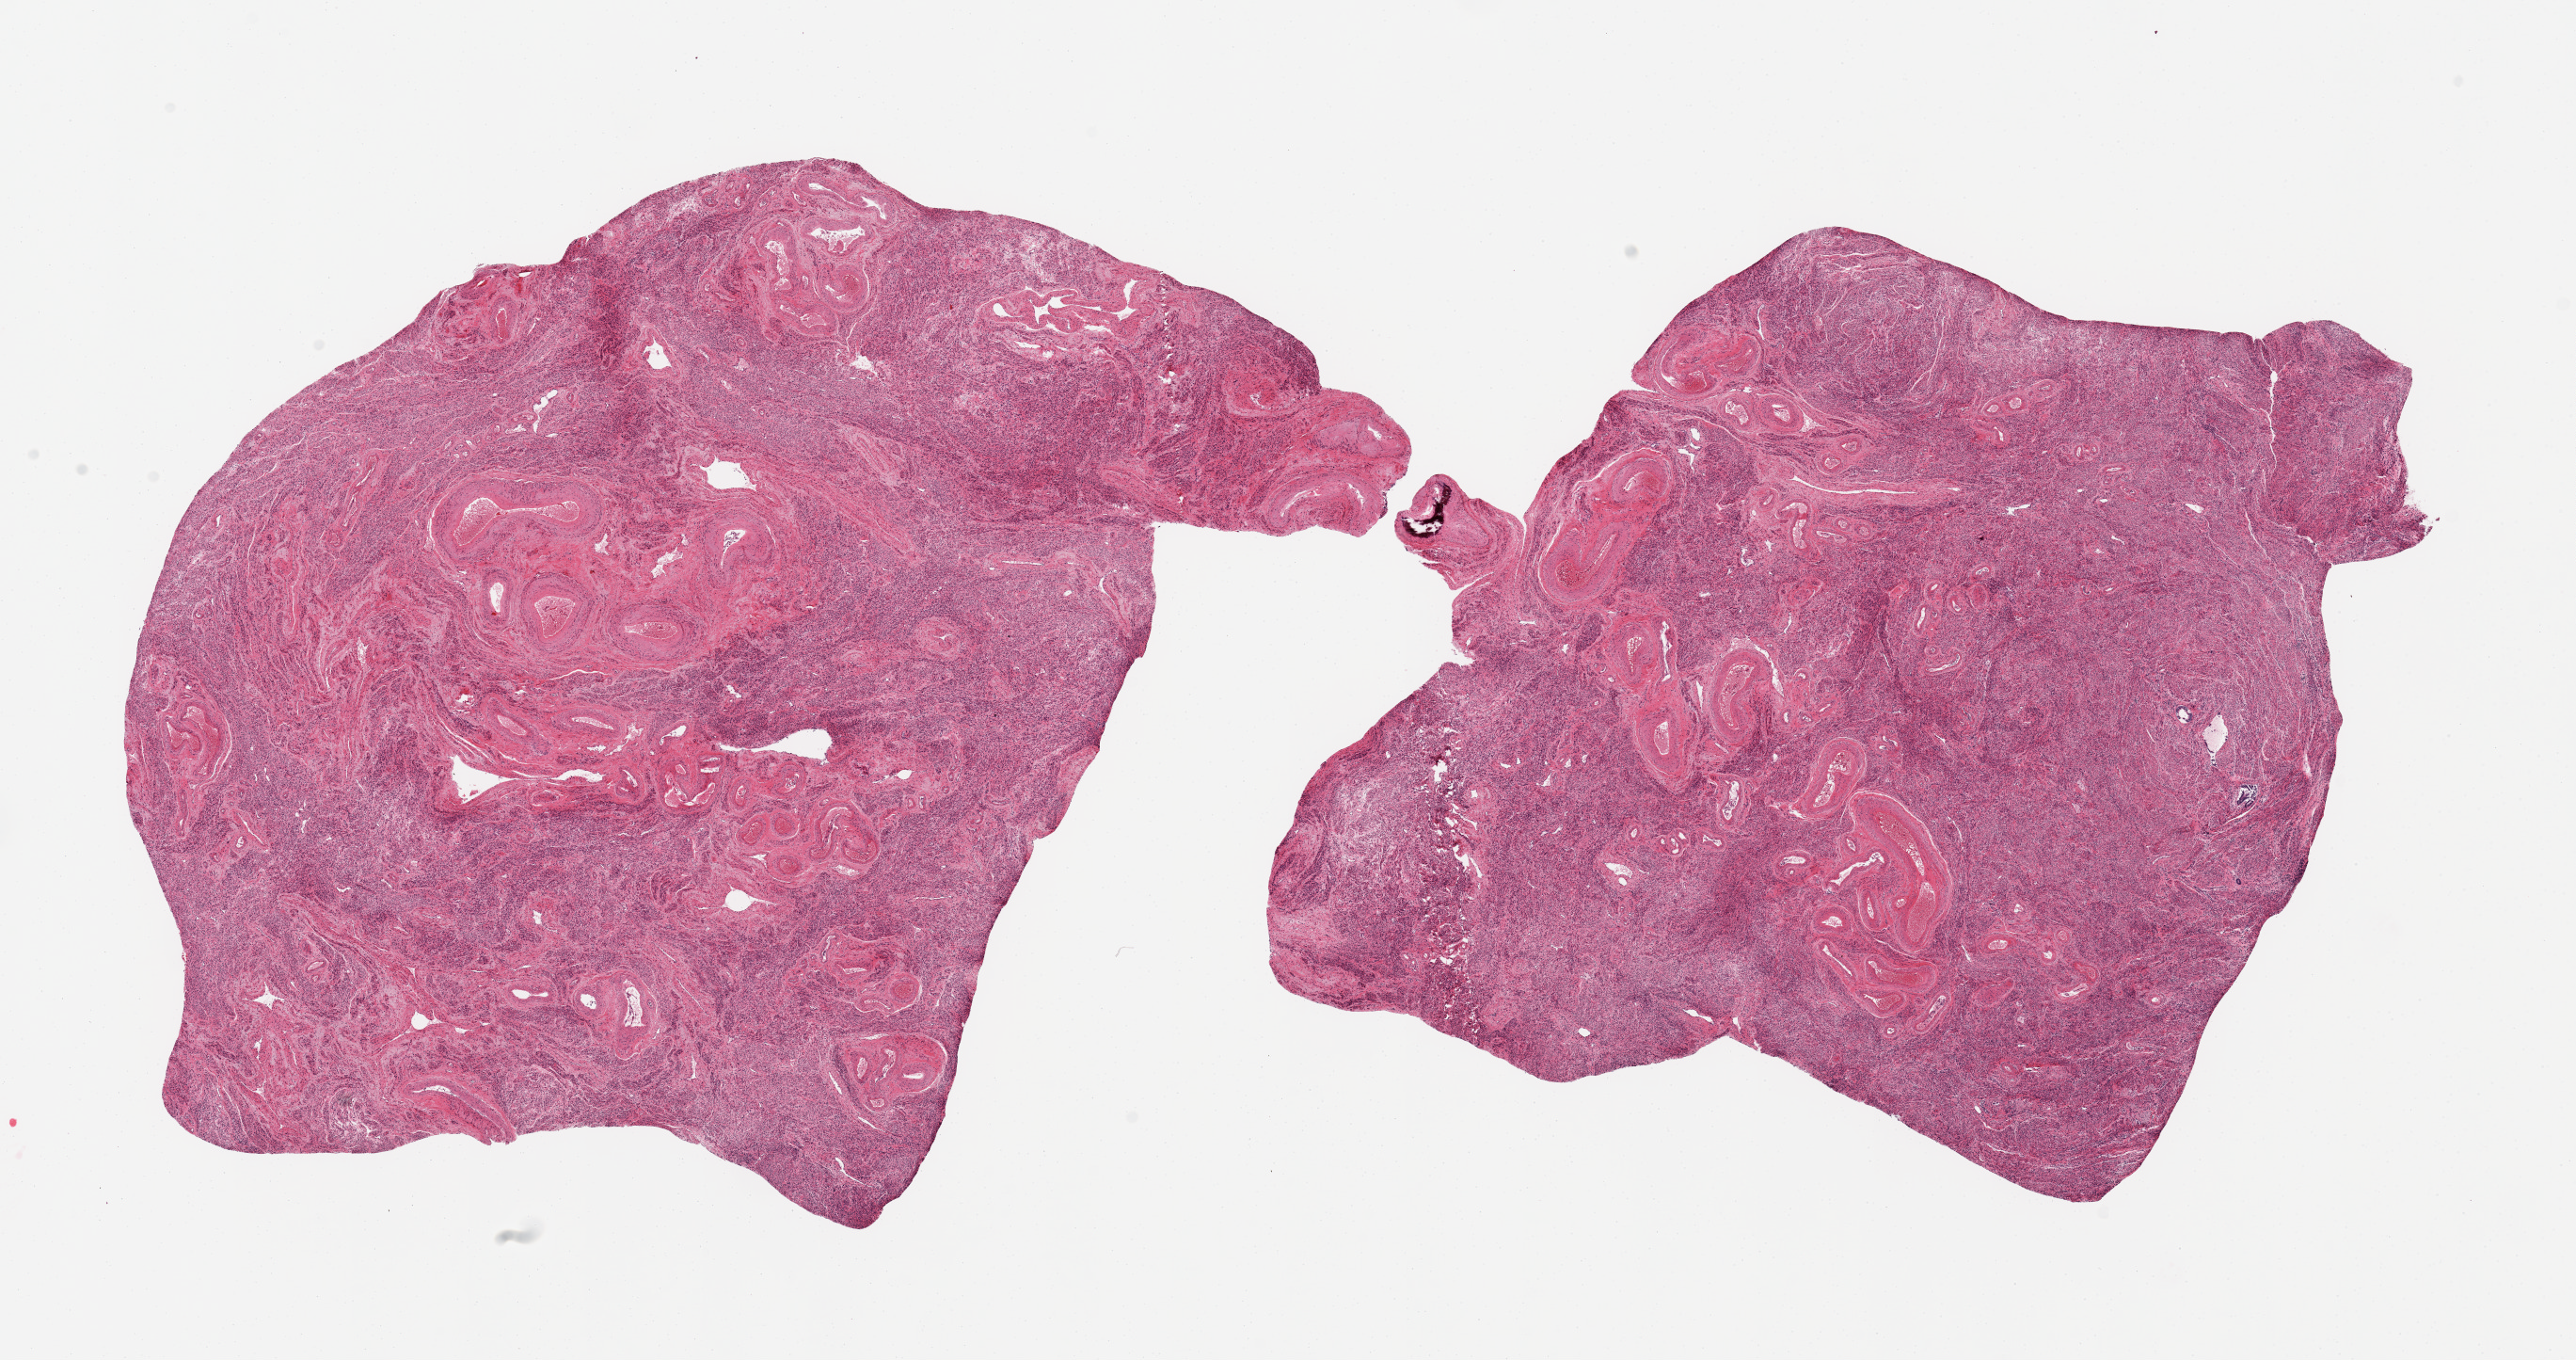
Whole-slide image, haematoxylin and eosin stain — whole scanned area (about 21.7 x 11.4 mm) shown as a low-resolution overview. PAXgene-fixed, paraffin-embedded tissue. Section of uterus (target tissue). Tissue donor sample. Donor: female.
- reviewer comment on this tissue sample: 2 pieces; predominantly myometrium with prominent thick walled vessels and remnant of a few inactive glands with sloughing epithelium; focal medial vascular calcification